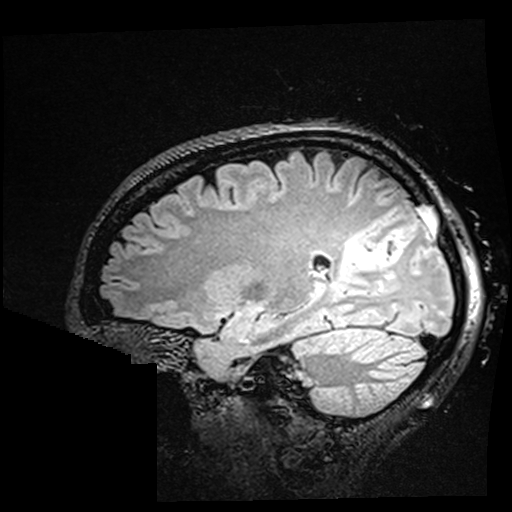
Brain MRI from a brain-tumour surgery series, one sagittal slice. Slice 115 of 176 in the series (ordered by position). T2 FLAIR. 1 mm slice thickness. 512 × 512 image matrix, field of view 250 × 250 mm. From the clinical record (not read from this slice): histopathology: Oligodendroglioma; WHO grade: 2; IDH mutation: yes.
Structures marked on this image (expert manual segmentation):
- residual tumour: bounding box <337,232,389,281> (left, top, right, bottom; pixels)